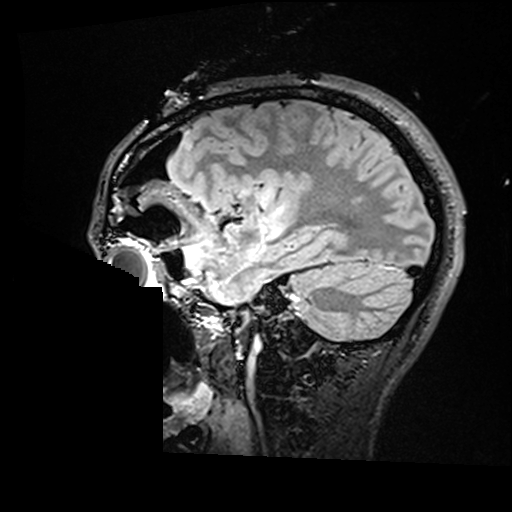
Brain MRI from a brain-tumour surgery series, one sagittal slice; position 118 of 176 along the scan axis; T2 FLAIR; 512 × 512 image matrix, field of view 250 × 250 mm. Case-level facts recorded for this patient, not image findings: histopathology: Astrocytoma; WHO grade: 2; IDH mutation: yes.
Structures marked on this image (expert manual segmentation):
- residual tumour: bounding box <260,189,284,226> (left, top, right, bottom; pixels)